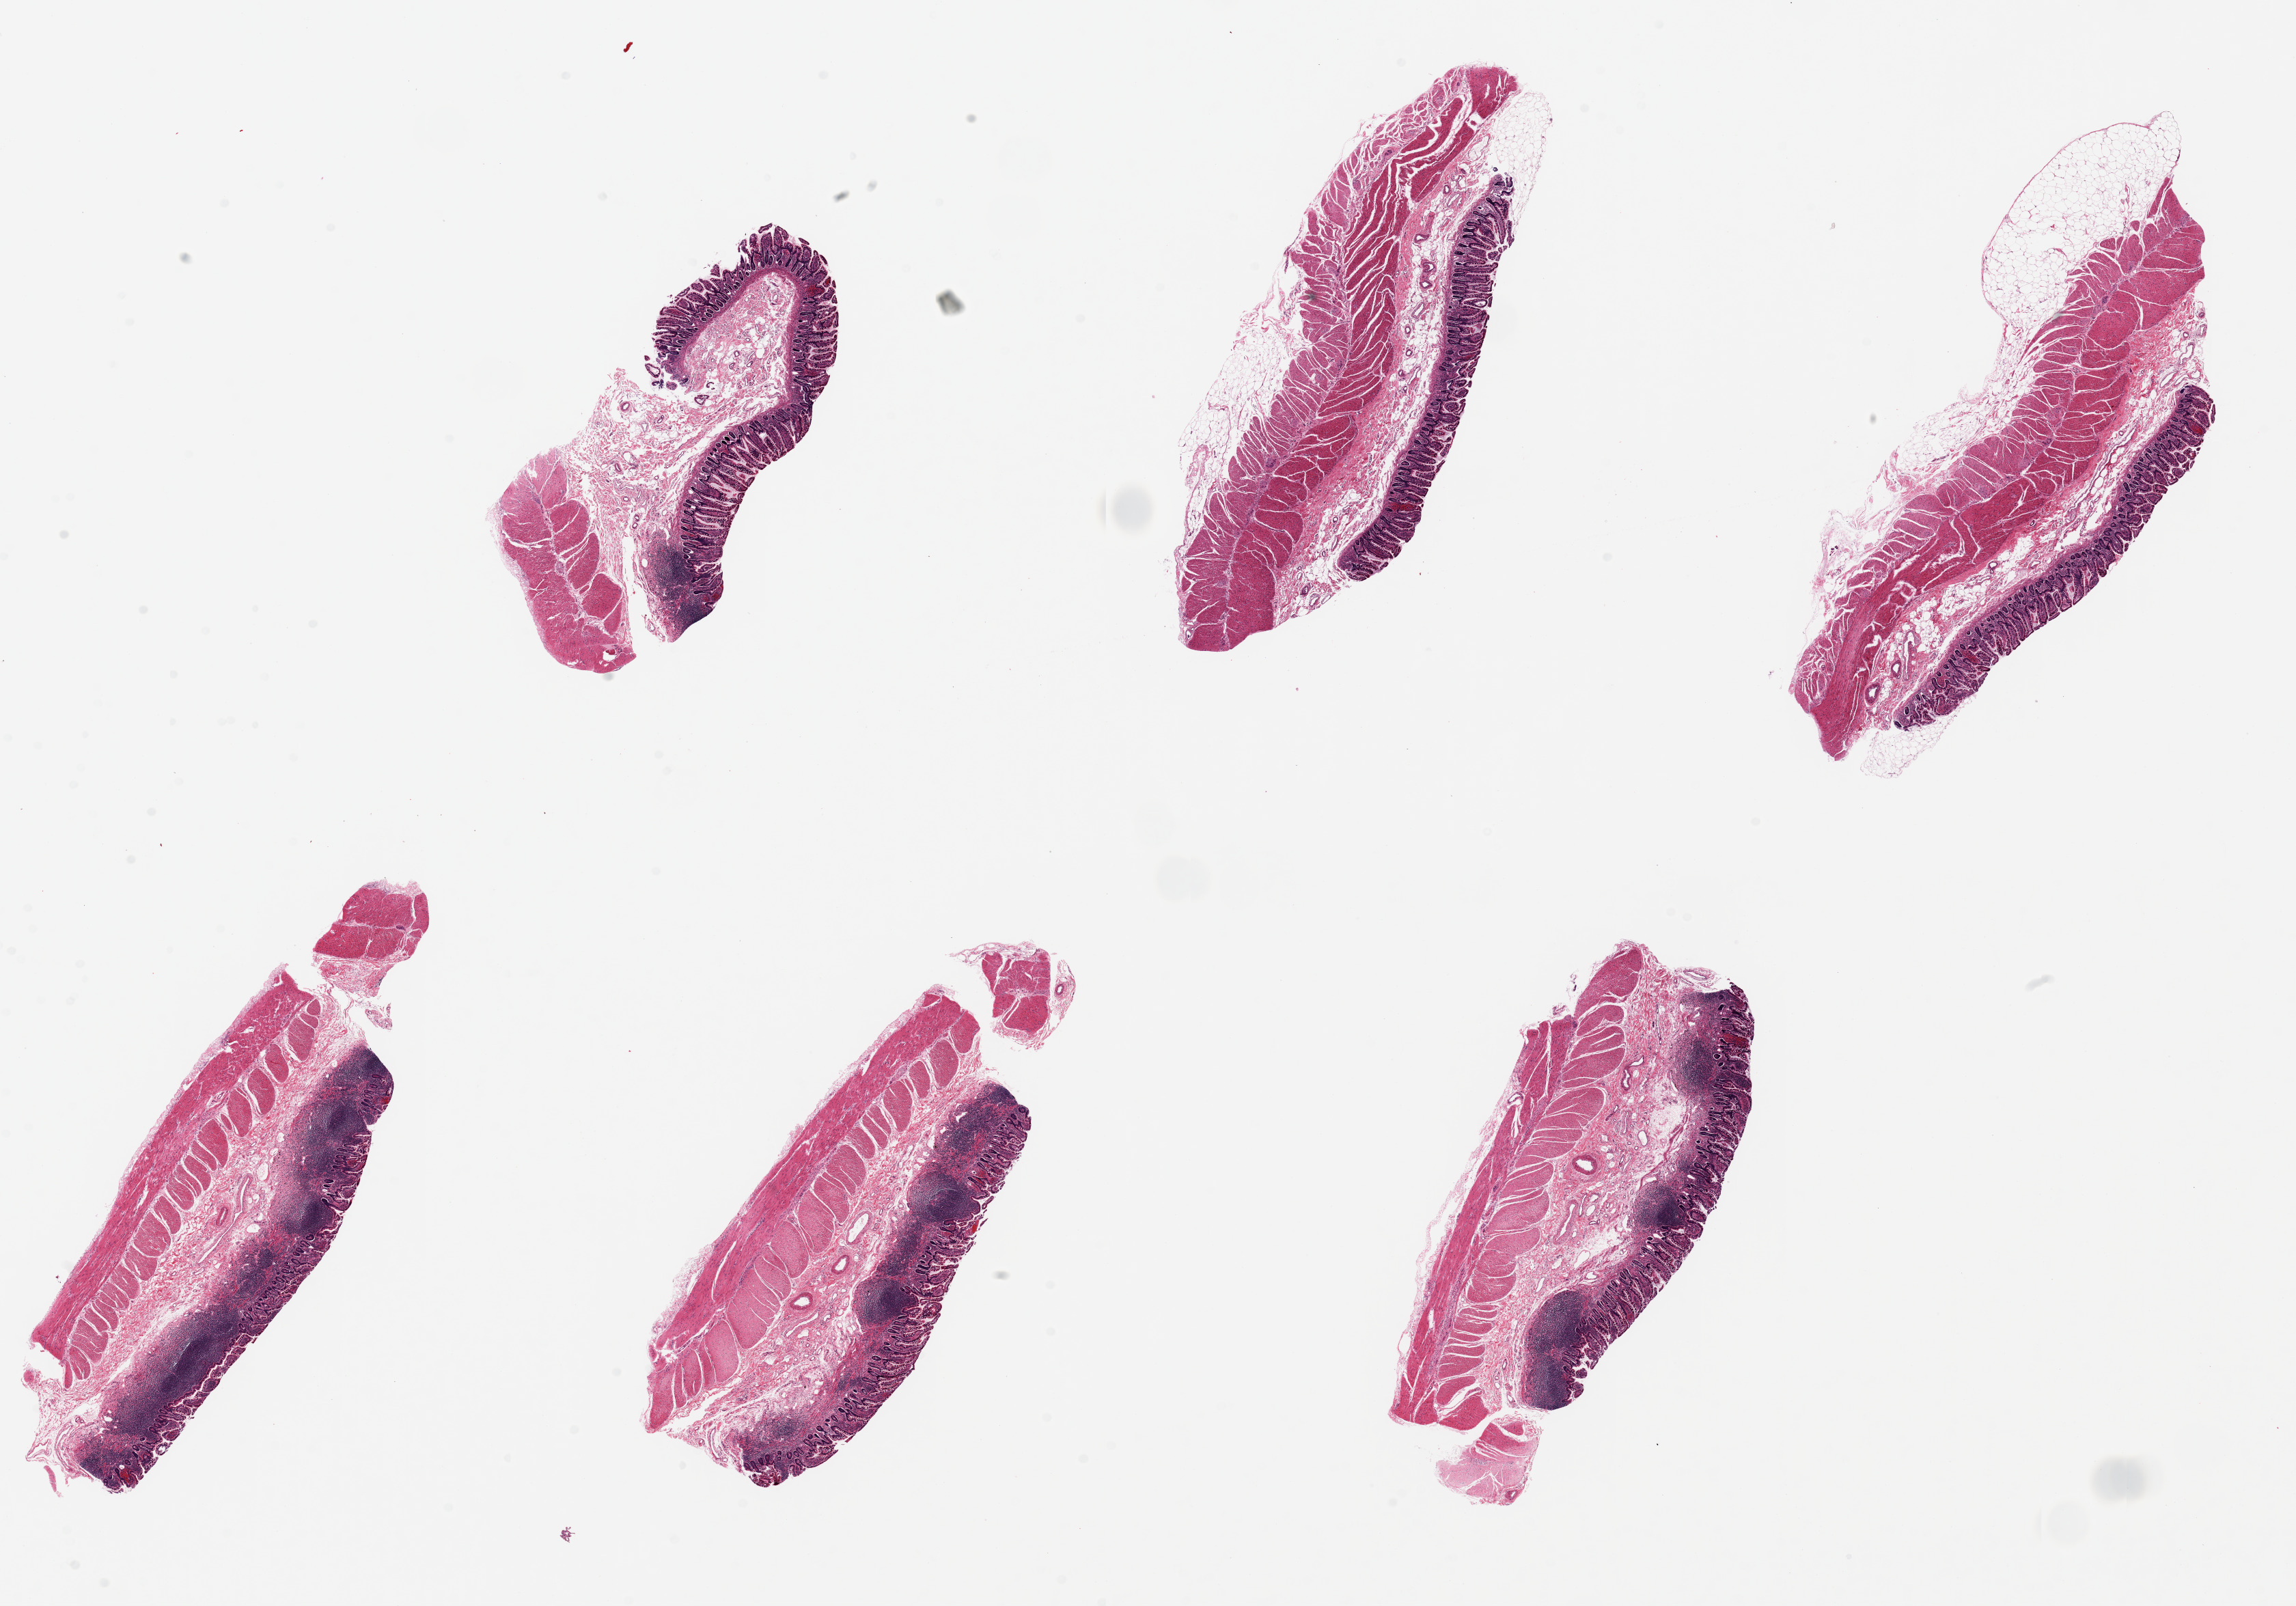
Whole-slide image, haematoxylin and eosin stain — a low-resolution overview of the entire scanned area, about 26.6 x 18.6 mm; PAXgene-fixed, paraffin-embedded tissue; target tissue: ileum; donor tissue sample. Donor sex: male.
• reviewer comment on this tissue sample: 6 pieces, 8x4mm; up to Muscularis propria in all 6 pieces (not target tissue); lymphoid tissue in 4 of 6